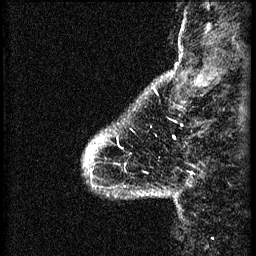
Breast MRI (dynamic contrast-enhanced), one sagittal slice. Position 5 of 60 along the scan axis. 3 images stored at this slice position (order not interpretable as contrast timing). 1.5 T. TE 4.2 ms, TR 8.2 ms. 2.2 mm slice thickness. 256 × 256 image matrix. Female patient, age 41 years.
Annotated regions visible in this slice (semi-automatically segmented with operator editing):
- analysis volume of interest (the breast-tissue region the enhancement analysis was run in; not a lesion): bounding box <85,130,157,197> (left, top, right, bottom; pixels)
- tumour enhancement mask (voxels above the 70 % enhancement threshold inside the analysis volume of interest): <87,138,103,157>